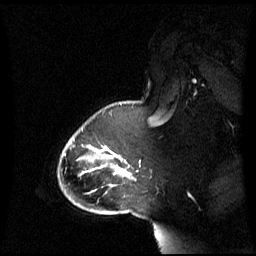
Breast MRI (dynamic contrast-enhanced), one sagittal slice; position 48 of 60 along the scan axis; dynamic contrast-enhanced series, image 2 of 3 at this slice position (ordered by acquisition); 1.5 T; TE 4.2 ms, TR 8.4 ms; 256 × 256 image matrix, field of view 270 × 270 mm. Patient: female, 43 years. From the clinical record (not read from this slice): setting: breast cancer imaged before/during neoadjuvant chemotherapy; receptor status: triple-negative.
Annotated regions visible in this slice (semi-automatically segmented with operator editing):
- analysis volume of interest (the breast-tissue region the enhancement analysis was run in; not a lesion): box from (x=65, y=118) to (x=143, y=198) px
- tumour enhancement mask (voxels above the 70 % enhancement threshold inside the analysis volume of interest): (x=93, y=146)–(x=130, y=192)